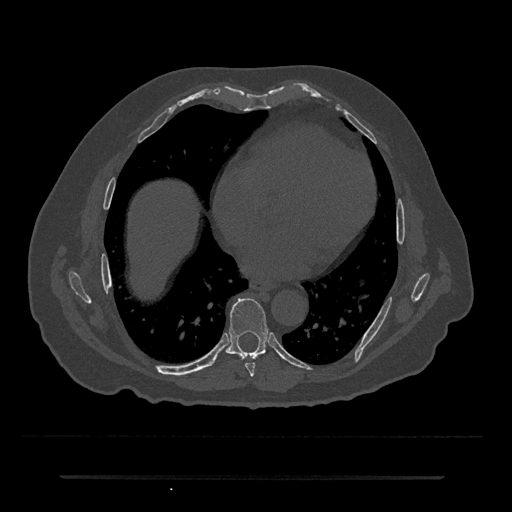
CT including the spine, one axial slice; slice 351 of 797 in the series (ordered by position); reconstruction kernel Br40s/3; 120 kVp; bone window (W 1800 / L 400 HU); 0.5 mm slice thickness; 512 × 512 image matrix, field of view 437 × 437 mm. Male patient, age 69 years. Case-level facts recorded for this patient, not image findings: primary cancer: prostate.
Annotated regions visible in this slice (semi-automatic segmentation, software-assisted and operator-edited):
- T7 vertebra: bounding box <245,363,255,377> (left, top, right, bottom; pixels)
- T8 vertebra: <225,298,268,360>